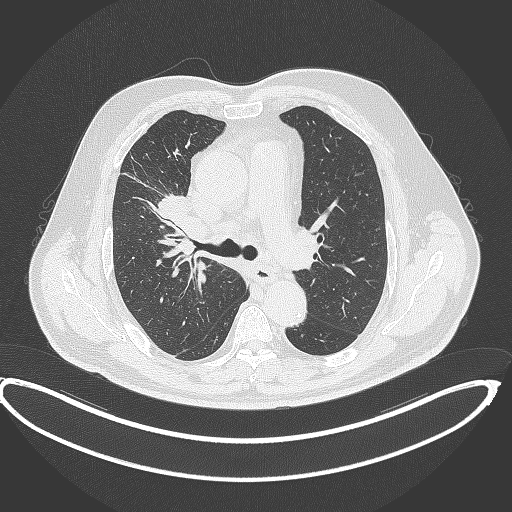
Chest CT, one axial slice; position 264 of 390 along the scan axis; reconstruction kernel B70f; lung window (W 1500 / L -600 HU); 512 × 512 image matrix. Patient: male, 62 years. Case-level facts recorded for this patient, not image findings: clinical TNM (as recorded): T1c N3 M1c.
Outlined on this slice (rectangle marked by the reading radiologist):
- lung tumour (recorded histology: adenocarcinoma): bounding box [x1, y1, x2, y2] px = [156, 191, 202, 240]